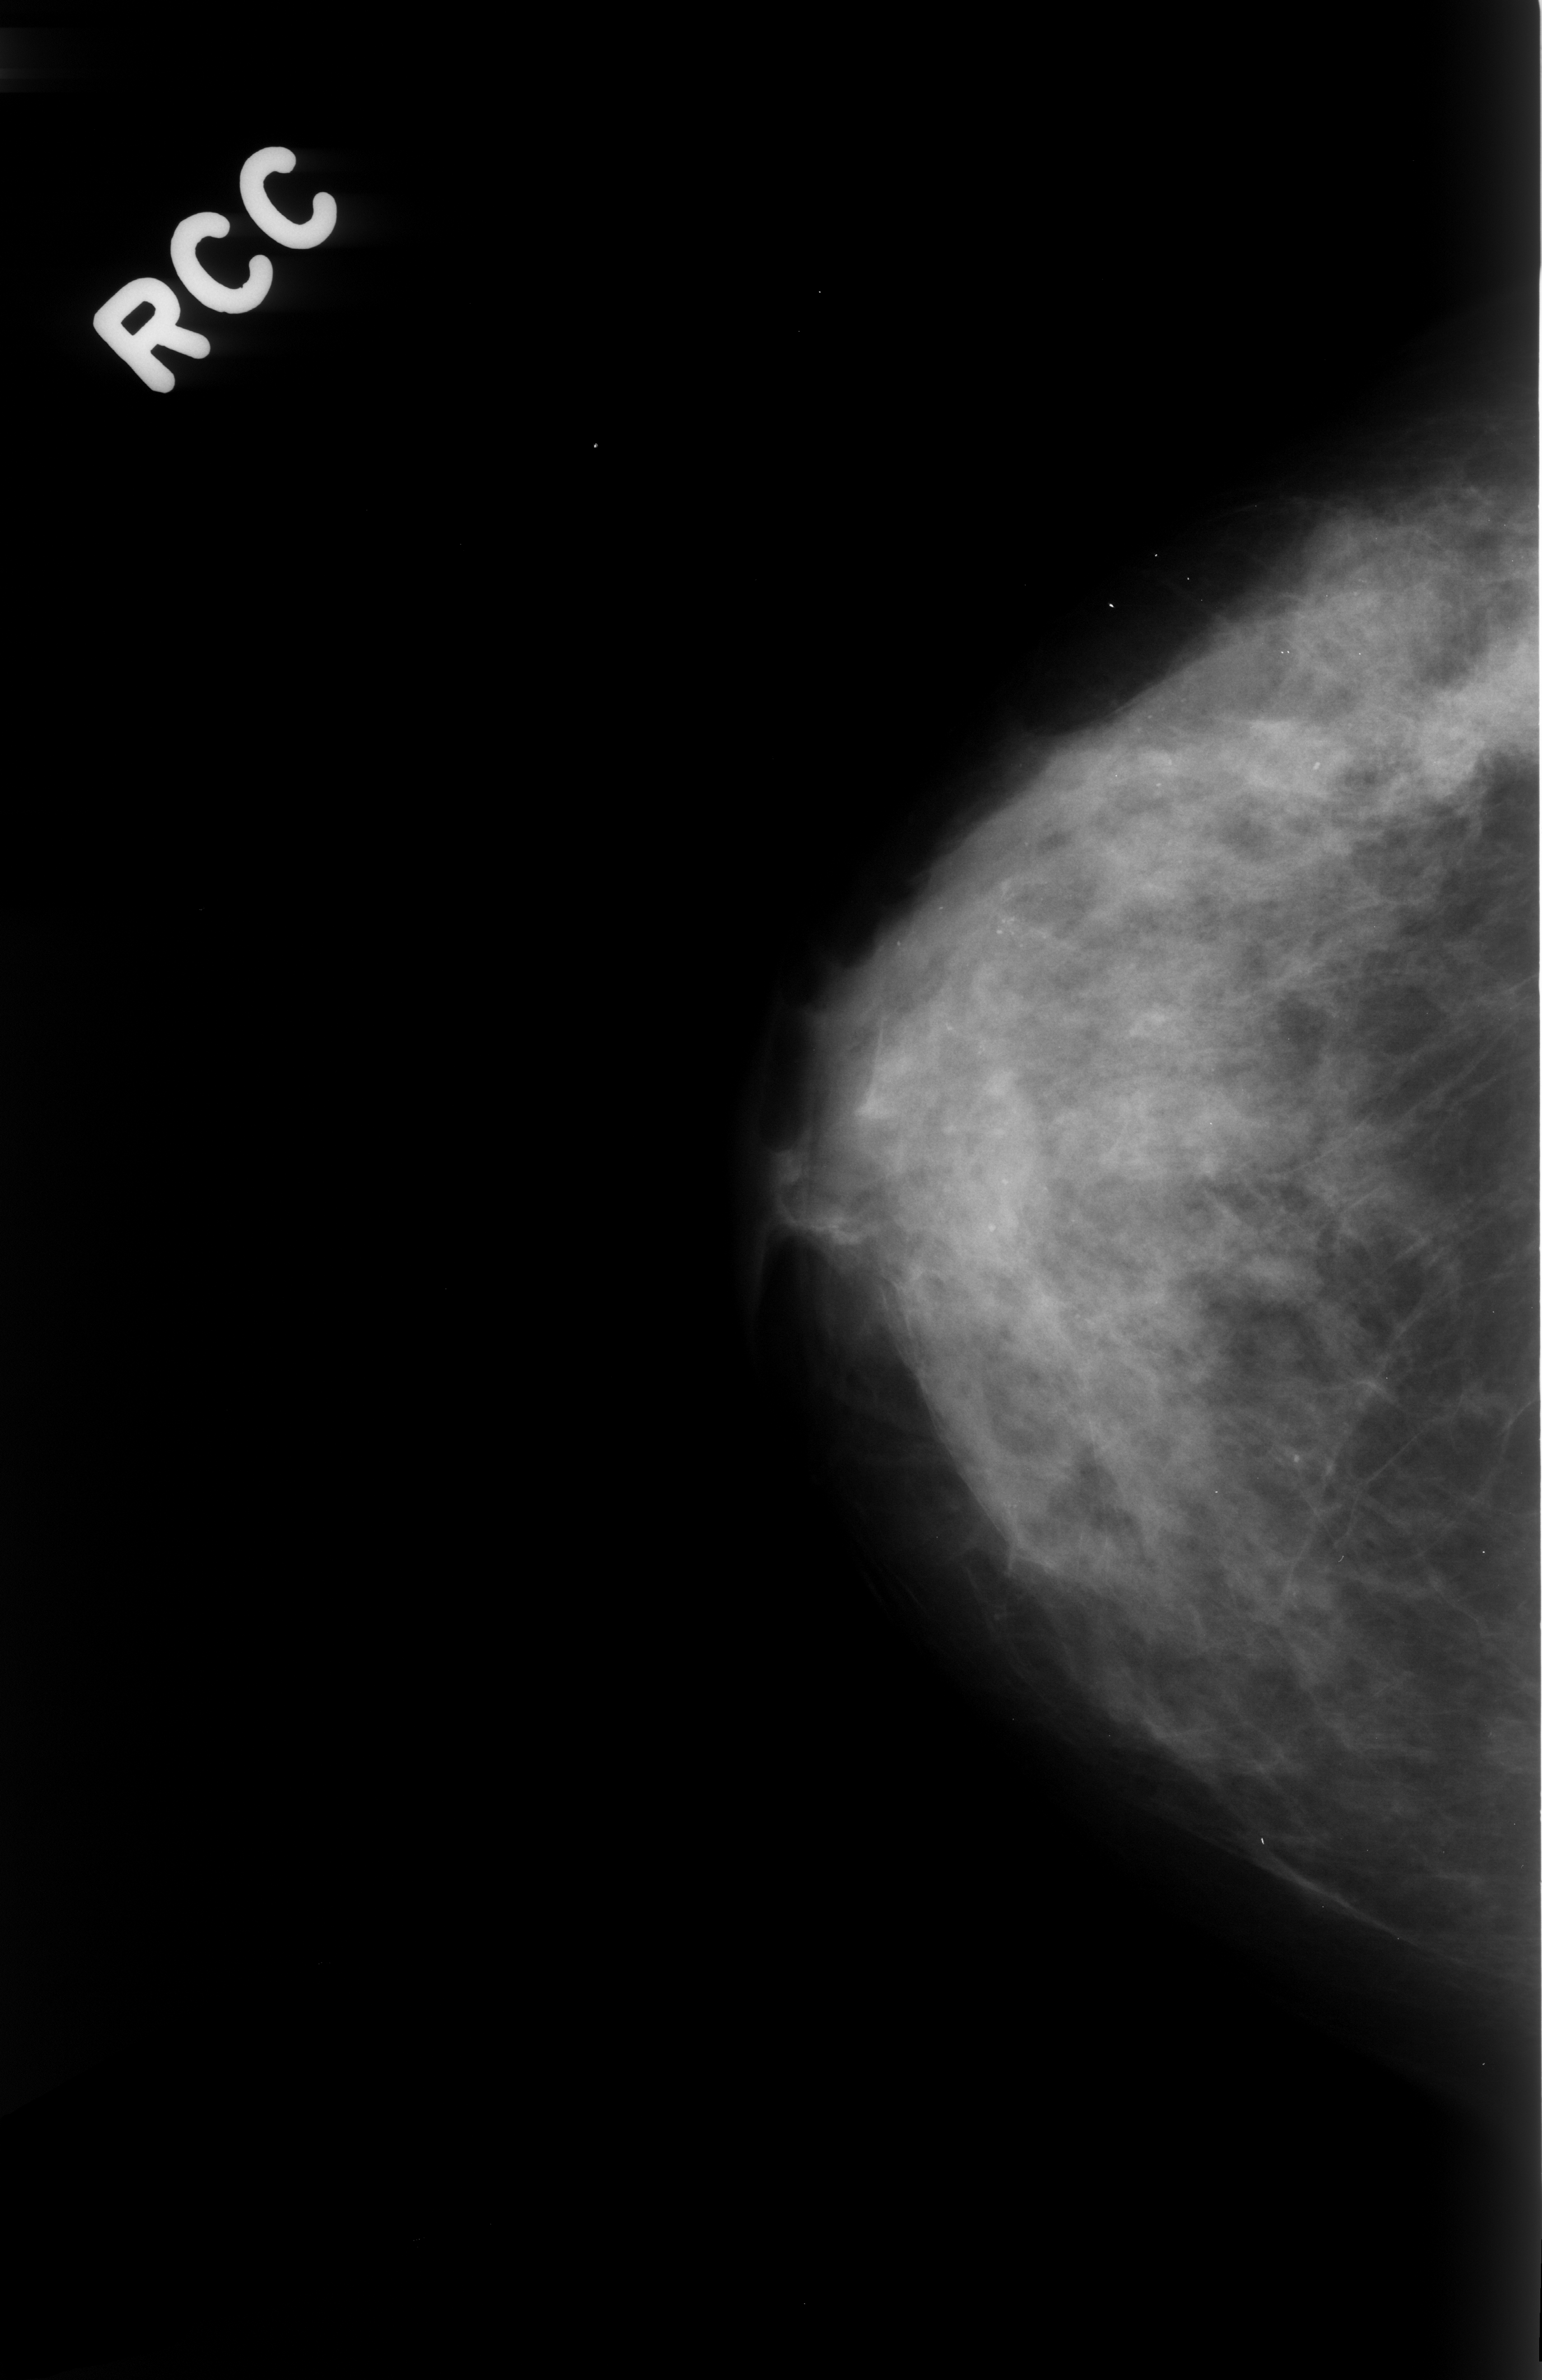
Mammogram (digitized film), right breast, craniocaudal (CC) view.
- Calcifications, morphology pleomorphic, distribution diffusely scattered; BI-RADS assessment category 3; subtlety rating 3 on a 1 (subtle) to 5 (obvious) scale; pathology (as recorded): benign.